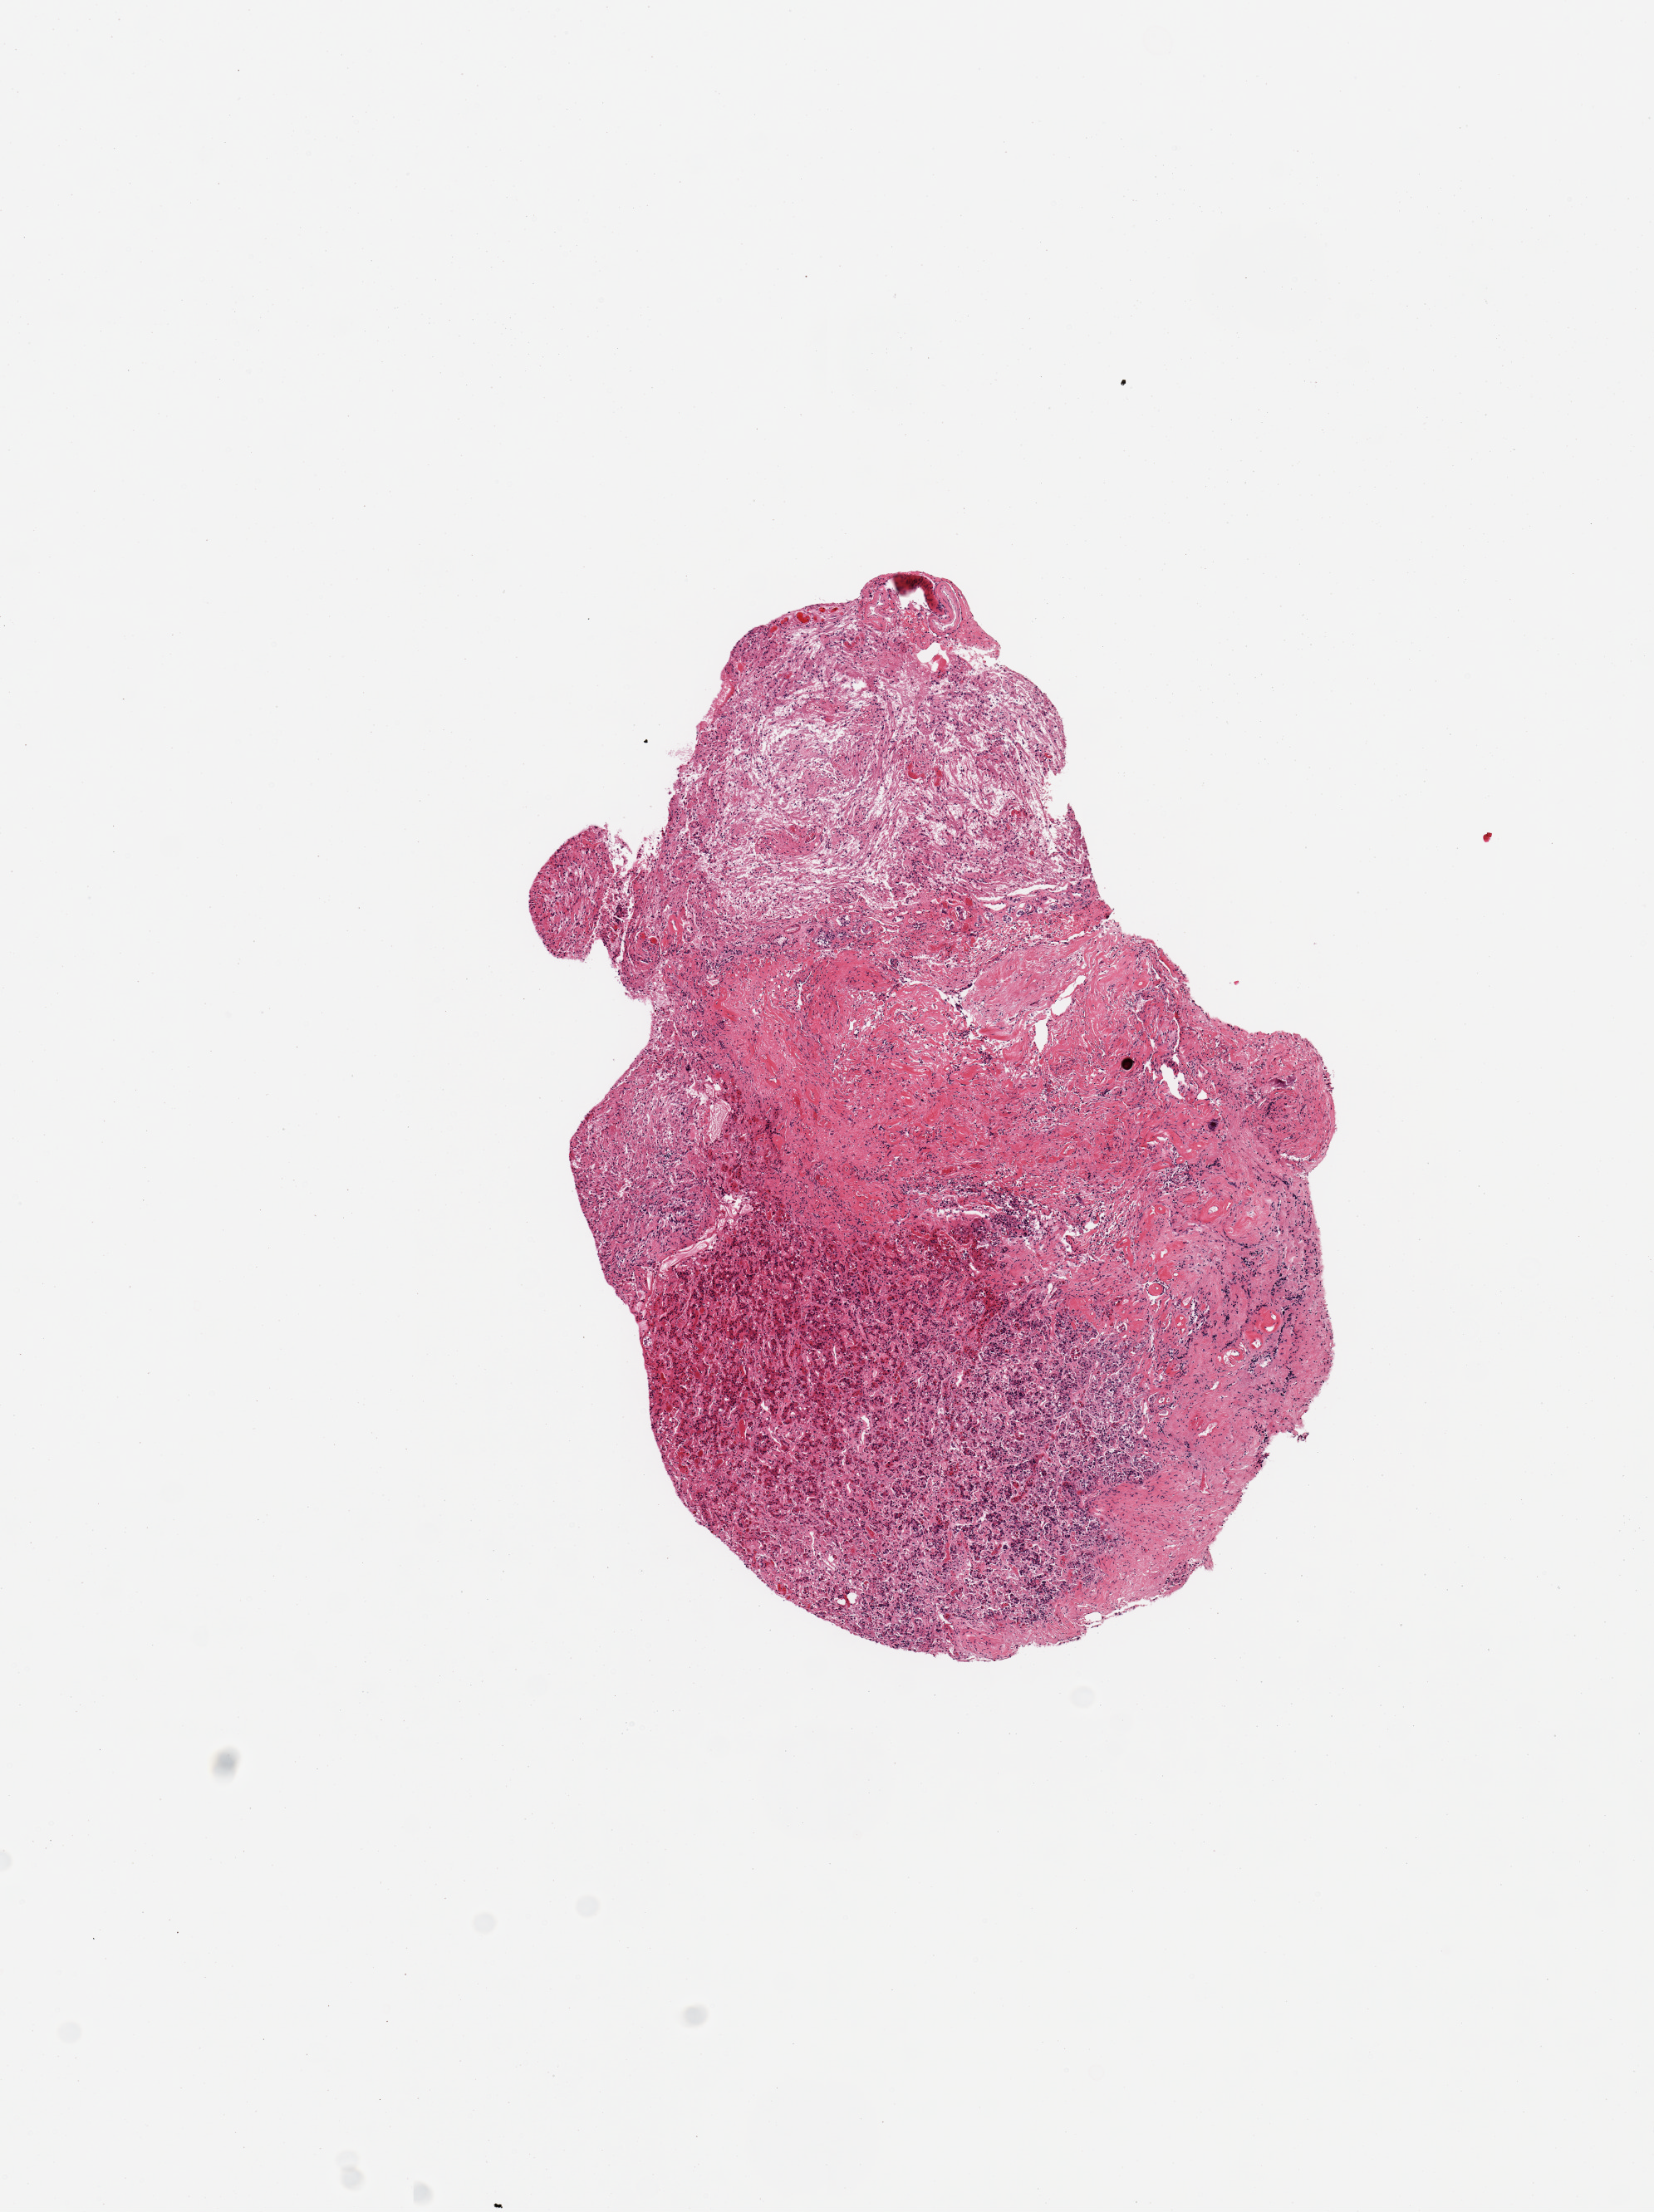
Whole-slide image, haematoxylin and eosin stain, brightfield — a low-resolution overview of the entire scanned area, about 7.9 x 10.5 mm (acquisition: 20x scan); PAXgene-fixed, paraffin-embedded tissue; section of pituitary (target tissue); tissue donor sample. Donor sex: male.
Reviewer comment on this tissue sample: 1 piece, pituitary, ~50% adenohypophysis, ~50% neurohypophysis.